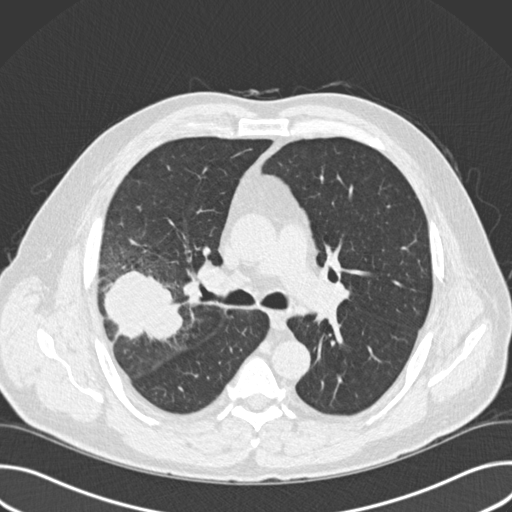
Low-dose screening chest CT, one axial slice. Slice 101 of 157 in the series (ordered by position). Reconstruction kernel B30f. 120 kVp. Lung window (W 1500 / L -600 HU). 512 × 512 image matrix, field of view 380 × 380 mm.
Outlined on this slice (manually delineated by an expert):
- lesion 1 (tumor, upper lobe of right lung): bounding box [x1, y1, x2, y2] px = [104, 270, 183, 342]